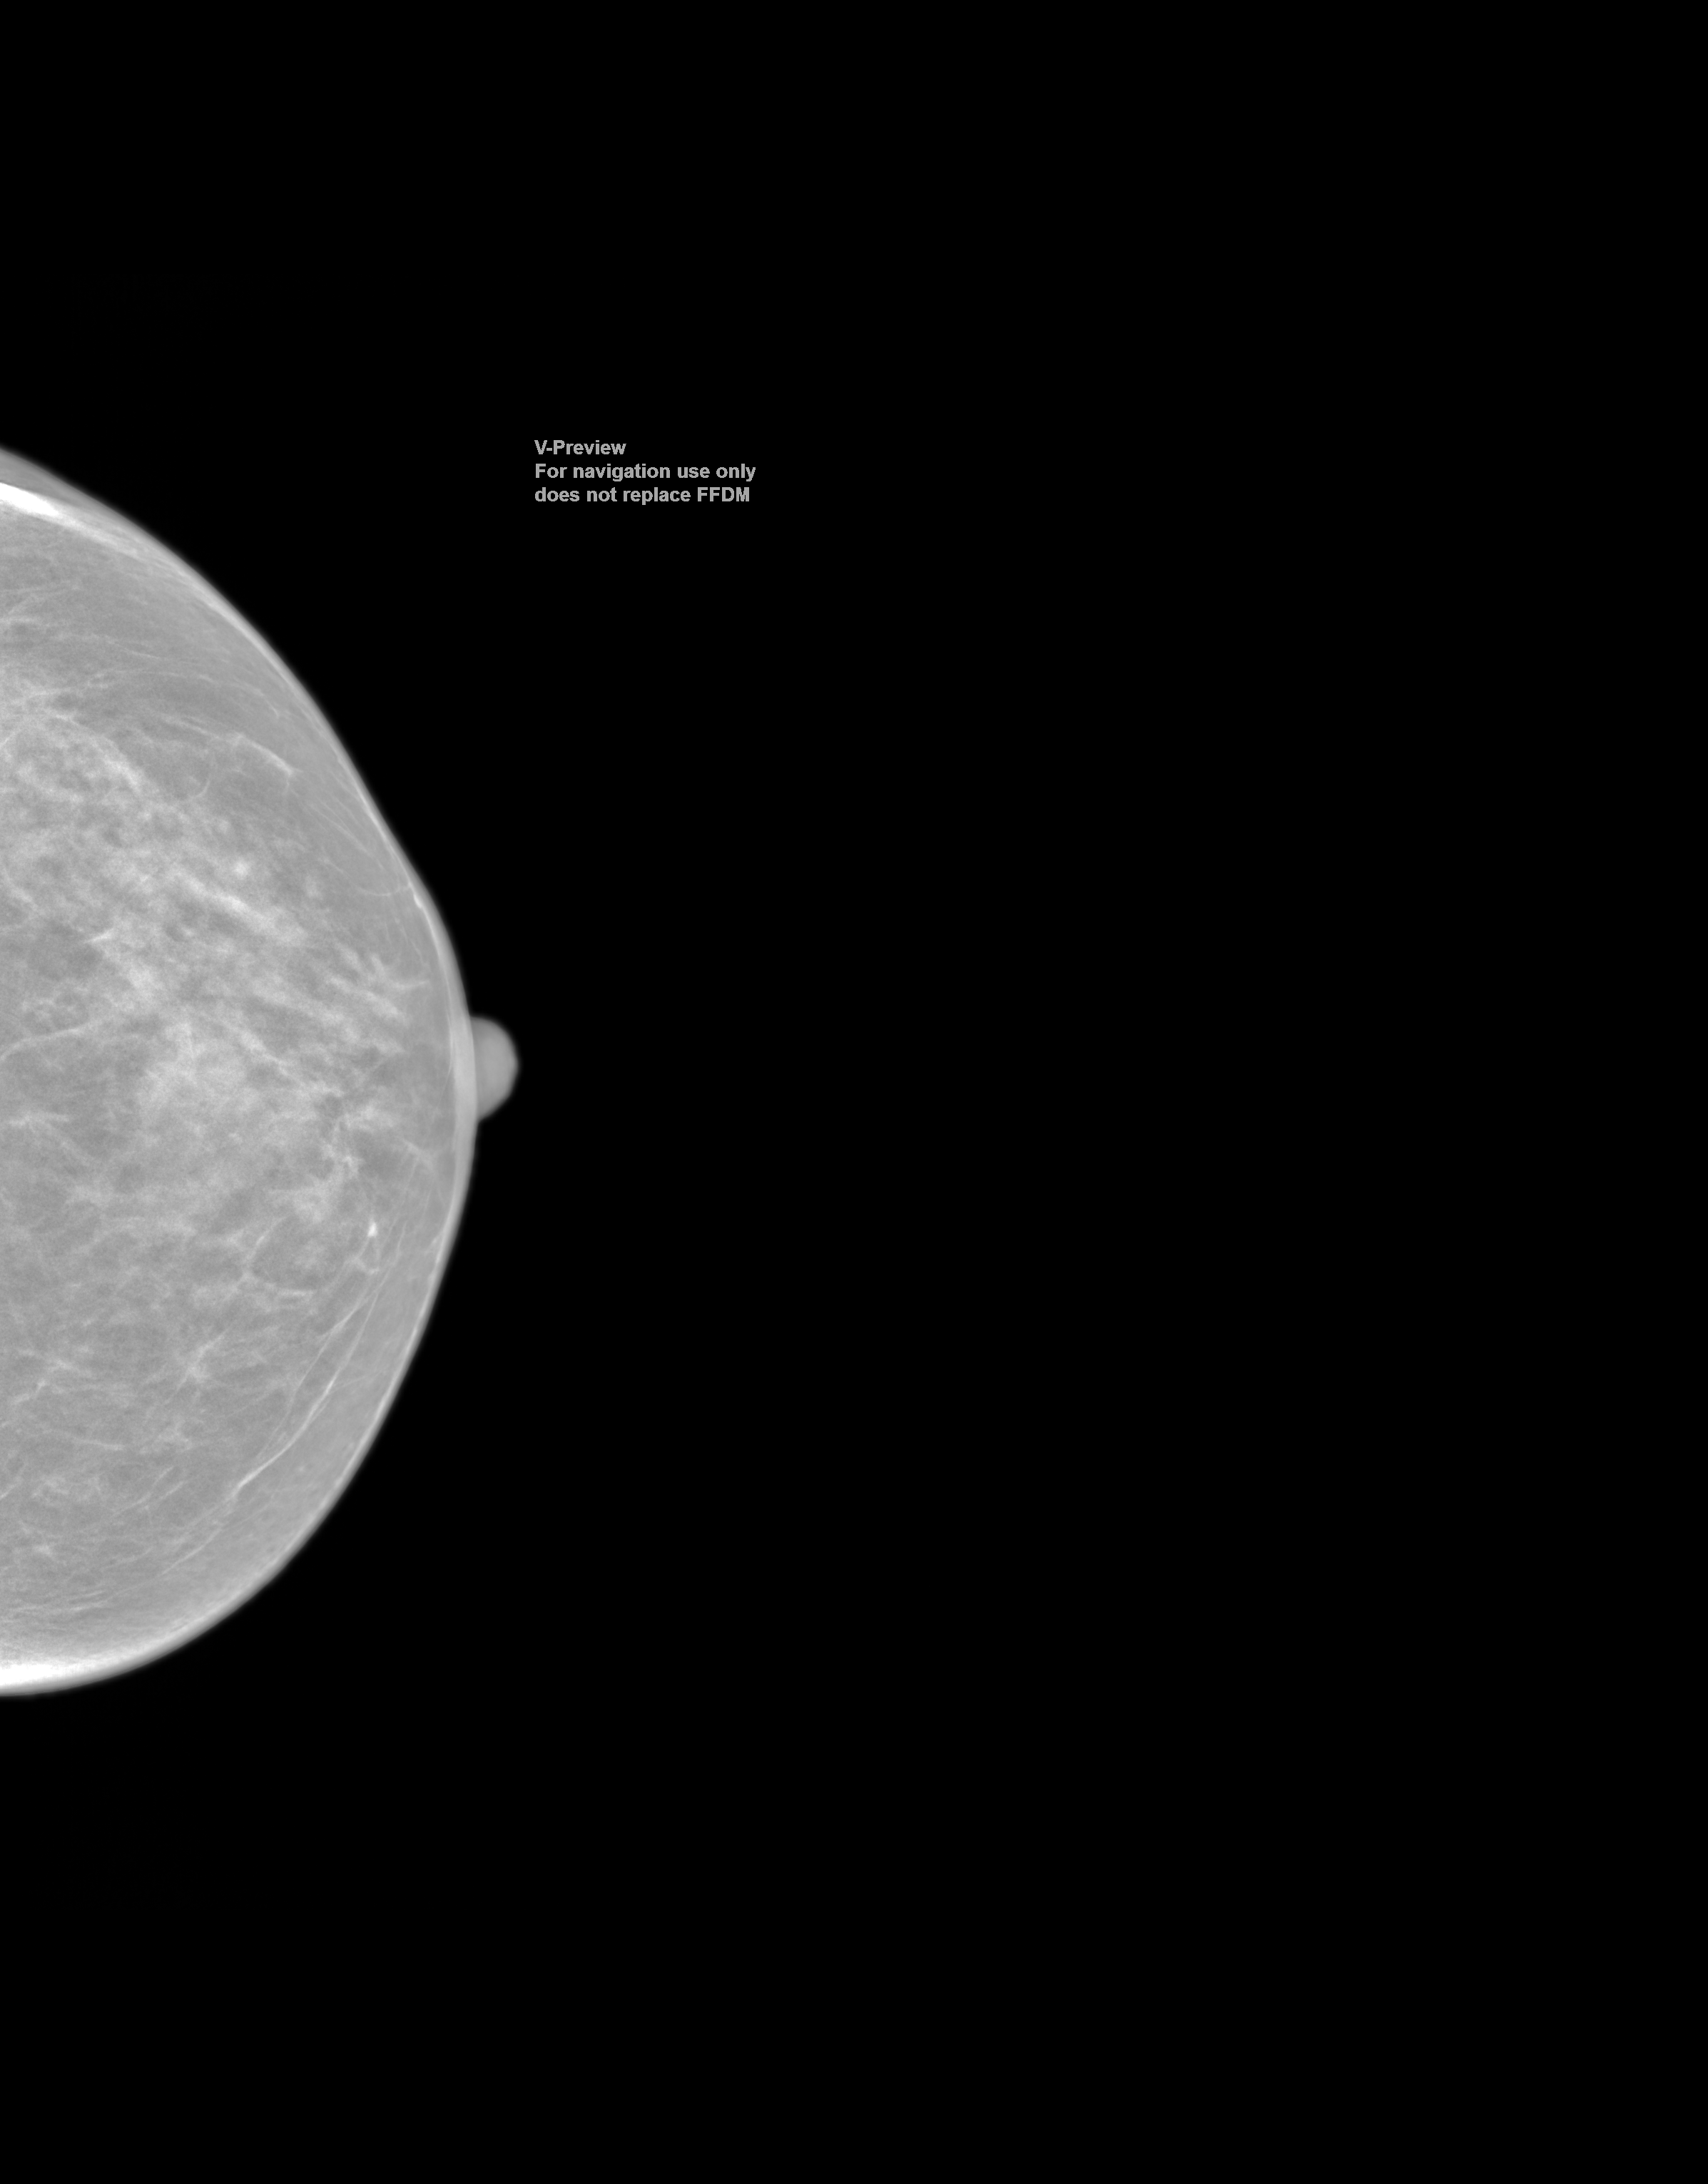
Synthetic 2-D view generated from a tomosynthesis acquisition (not an FFDM exposure); left breast; cranio-caudal projection; screening examination. Patient aged 61 years (female).
Breast density at the screening exam (both breasts): heterogeneously dense (BI-RADS density category c). Final BI-RADS assessment for this screening round (tomosynthesis exam, both breasts): category 1. Recall: no recall after this screen.